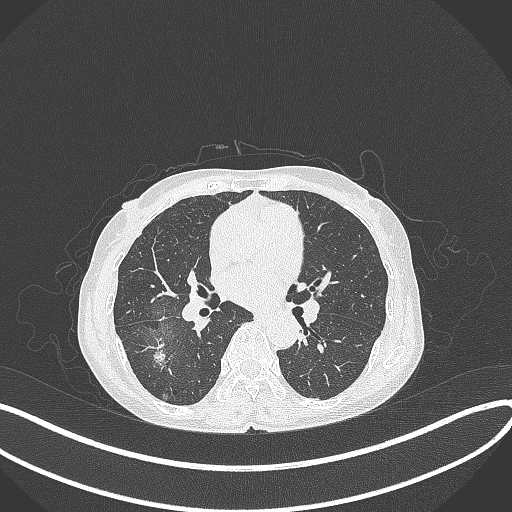
Chest CT, one axial slice; position 203 of 371 along the scan axis; reconstruction kernel B70f; 120 kVp; lung window (W 1500 / L -600 HU); 1 mm slice thickness; 512 × 512 image matrix, field of view 400 × 400 mm. Patient: female, 69 years. Case-level facts recorded for this patient, not image findings: clinical TNM (as recorded): T1b N0 M0.
Structures marked on this image (rectangle marked by the reading radiologist):
- lung tumour (recorded histology: adenocarcinoma): bounding box (x1, y1, x2, y2) in pixels: (148, 336, 171, 370)